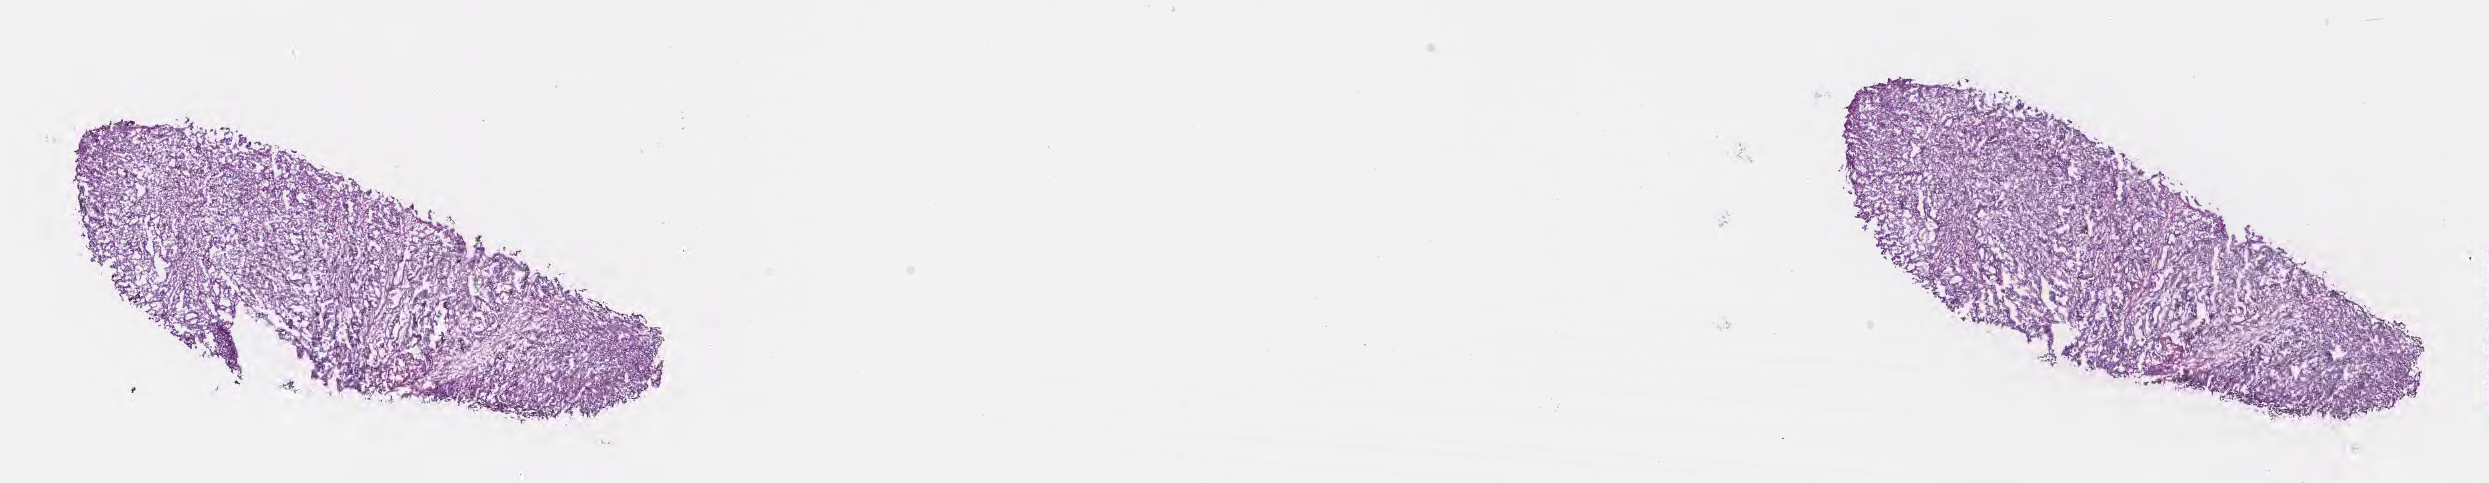
Whole-slide image, hematoxylin and eosin (H&E) stain — low-resolution overview of the scanned area, about 20.1 x 3.9 mm; frozen section; specimen: primary tumor; site: stomach. Patient: male, age at initial diagnosis 56 years. Tumor grade: G3 (poorly differentiated). Slide review estimates, as recorded: tumor cells 100%, tumor nuclei 90%, stromal cells 0%, necrosis 0%, normal cells 0%. Infiltration values recorded for this section: lymphocyte infiltration 0%, monocyte infiltration 0%, neutrophil infiltration 0%.
AJCC pathologic stage: Stage IIIB. Diagnosis: Adenocarcinoma, NOS.